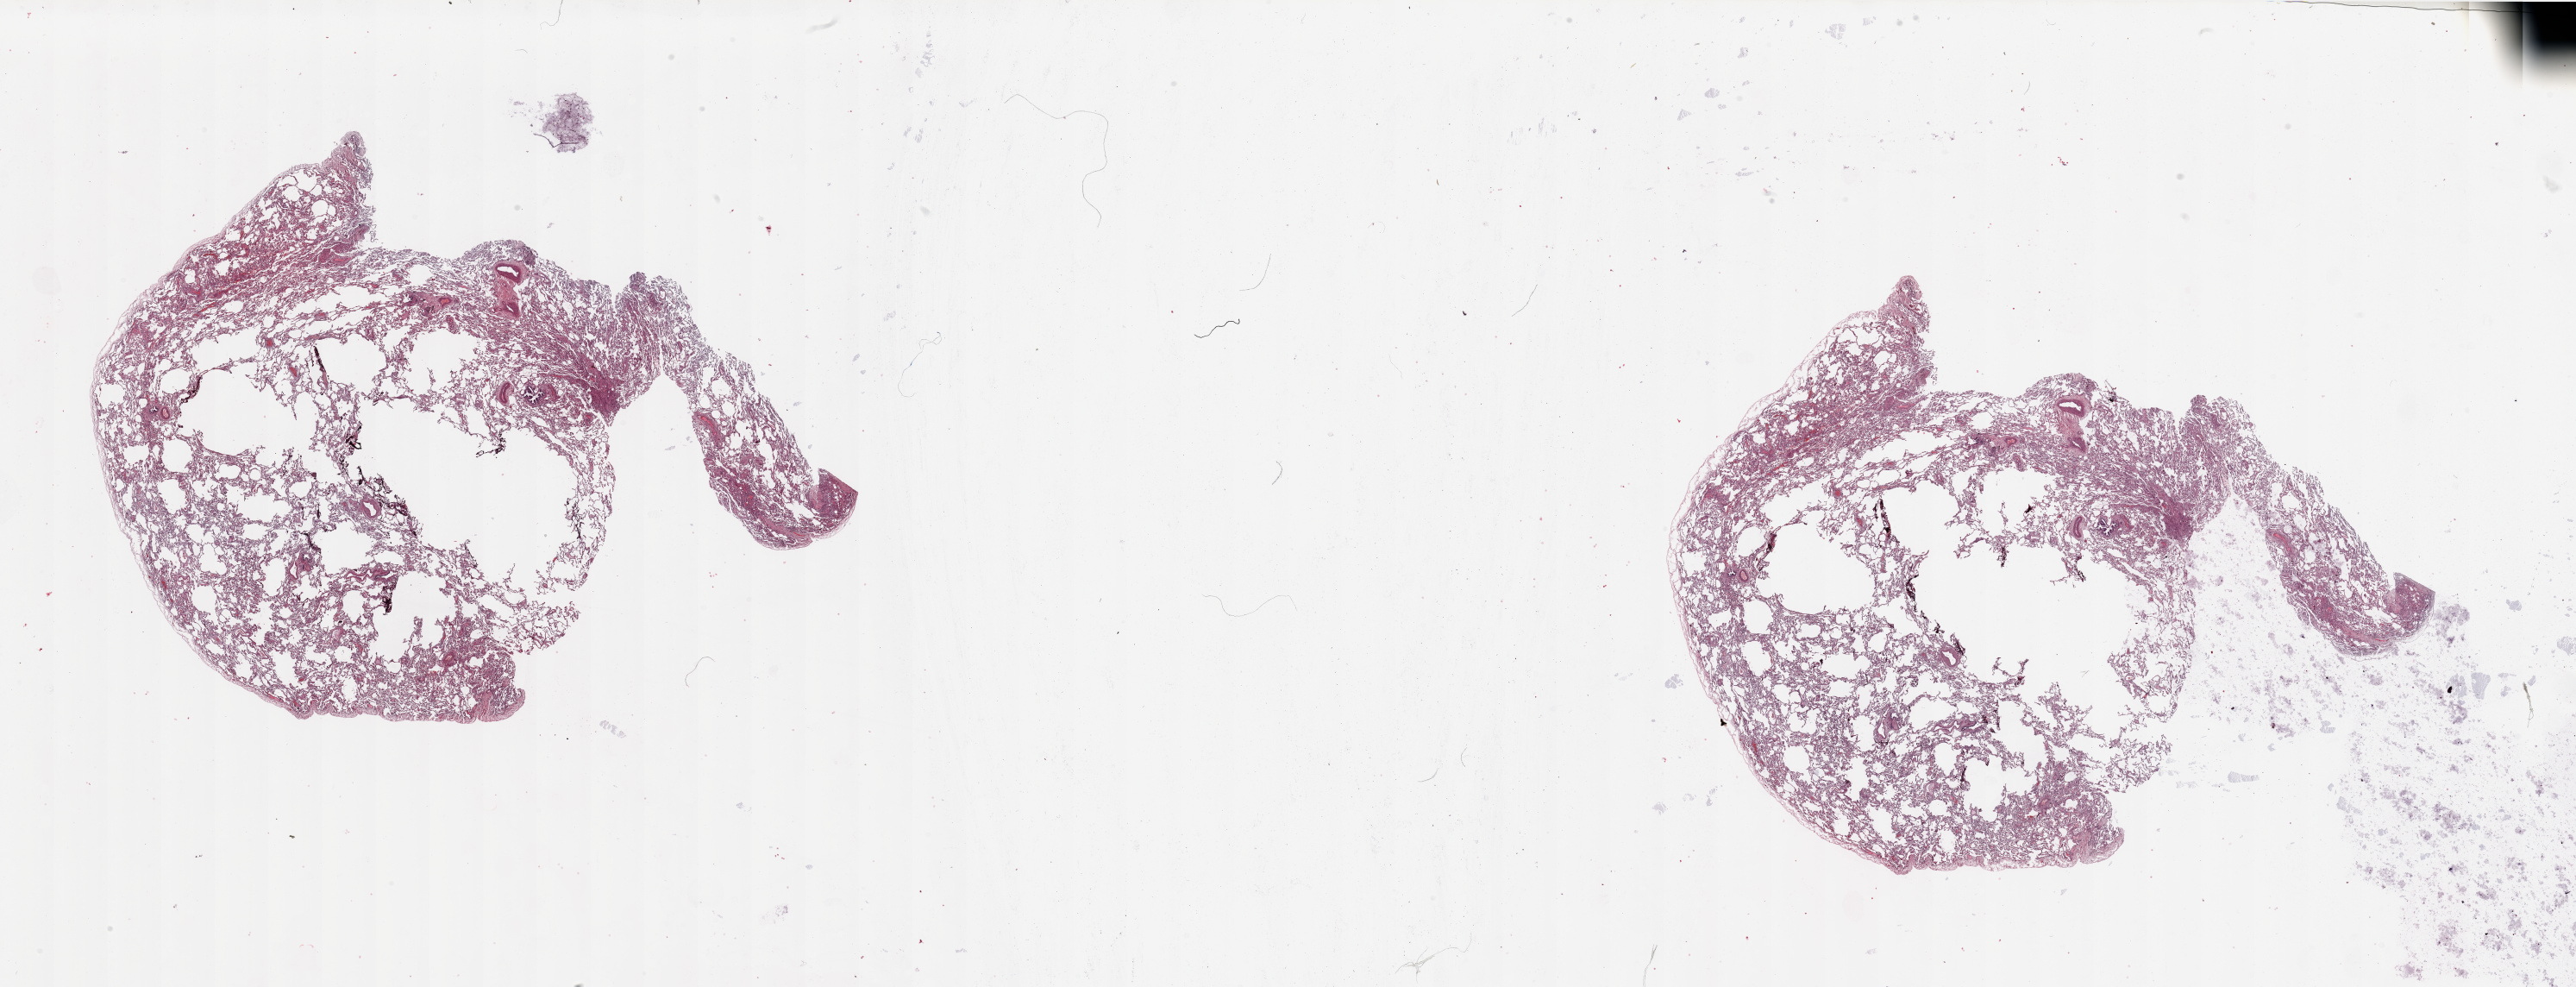
Digitized H&E-stained tissue section (whole slide), shown as a low-resolution overview of the whole scanned area (about 47.3 x 18.1 mm), lung, normal (non-tumour) tissue. 61-year-old female patient.
This section: normal (non-tumour) tissue from the same patient. Patient diagnosis: Adenocarcinoma, NOS.